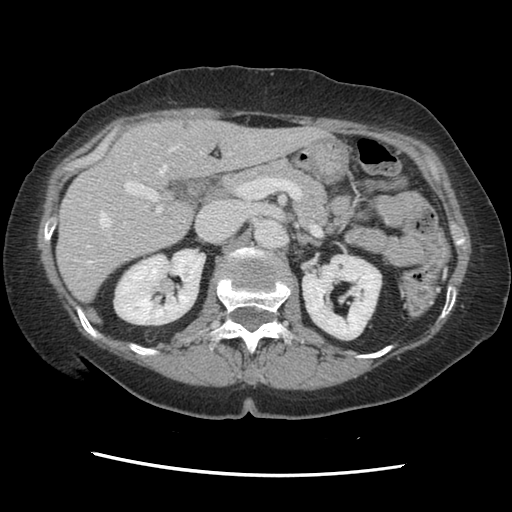
Contrast-enhanced abdominal CT, one axial slice; position 79 of 141 along the scan axis; soft-tissue window (W 400 / L 40 HU); 2.5 mm slice thickness; 512 × 512 image matrix, field of view 330 × 330 mm. Female patient, age 61 years. From the clinical record (not read from this slice): diagnosis: colorectal cancer liver metastases, imaged before liver resection; multiple liver metastases: no.
Outlined on this slice (manually delineated by an expert):
- hepatic veins: bounding box (x1, y1, x2, y2) in pixels: (89, 139, 290, 264)
- liver: (58, 121, 319, 300)
- planned liver remnant (the part of the liver to remain after resection): (58, 121, 319, 300)
- portal vein (with intrahepatic branches): (87, 162, 162, 247)
- liver metastasis: (182, 121, 192, 130)